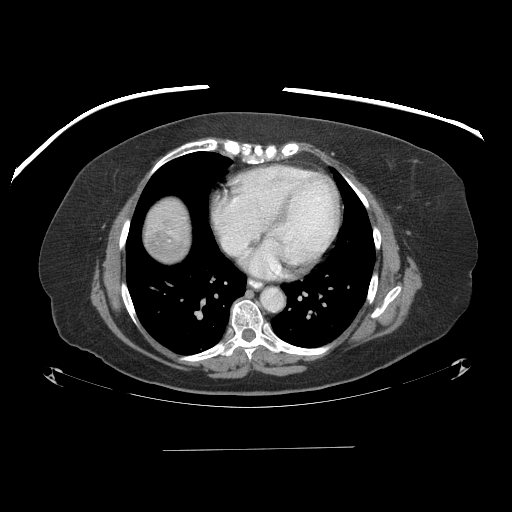
Contrast-enhanced abdominal CT (liver protocol), one axial slice. Slice 88 of 103 in the series (ordered by position). Reconstruction kernel STANDARD. 120 kVp. One of 2 acquisitions stored at this slice position. Soft-tissue window (W 400 / L 40 HU). 2.5 mm slice thickness. 512 × 512 image matrix, field of view 500 × 500 mm. From the clinical record (not read from this slice): diagnosis: hepatocellular carcinoma (patient treated with transarterial chemoembolisation; whether this scan precedes or follows treatment is not stated here); TNM stage (as recorded): Stage-IIIA; Child-Pugh class: A; tumour differentiation: poorly differentiated; tumour size: 5.2 cm.
Annotated regions visible in this slice (semi-automatically segmented with operator editing):
- liver parenchyma outside the tumour (the mass and vessels are separate outlines, so this box may not span the whole liver): bounding box (x1, y1, x2, y2) in pixels: (144, 198, 190, 262)
- mass: (146, 231, 182, 261)